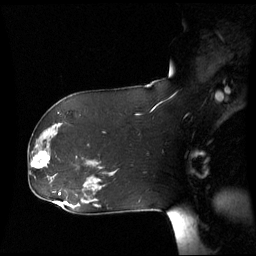
Breast MRI (dynamic contrast-enhanced), one sagittal slice; slice 36 of 60 in the series (ordered by position); dynamic contrast-enhanced series, image 2 of 3 at this slice position (ordered by acquisition); 1.5 T; TE 4.2 ms, TR 8.9 ms; 2.7 mm slice thickness; 256 × 256 image matrix. Female patient, age 61 years. From the clinical record (not read from this slice): setting: breast cancer imaged before/during neoadjuvant chemotherapy; receptor status: HR-positive, HER2-negative.
Outlined on this slice (semi-automatic segmentation, software-assisted and operator-edited):
- analysis volume of interest (the breast-tissue region the enhancement analysis was run in; not a lesion): bounding box <30,142,55,177> (left, top, right, bottom; pixels)
- tumour enhancement mask (voxels above the 70 % enhancement threshold inside the analysis volume of interest): <32,152,49,169>